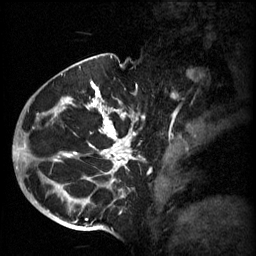
Breast MRI (dynamic contrast-enhanced), one sagittal slice. 3 images stored at this slice position (order not interpretable as contrast timing). 1.5 T. TE 4.2 ms, TR 11 ms. 256 × 256 image matrix. Patient: female, 51 years.
Structures marked on this image (semi-automatic segmentation, software-assisted and operator-edited):
- analysis volume of interest (the breast-tissue region the enhancement analysis was run in; not a lesion): bounding box [x1, y1, x2, y2] px = [48, 82, 161, 197]
- tumour enhancement mask (voxels above the 70 % enhancement threshold inside the analysis volume of interest): [53, 82, 139, 197]